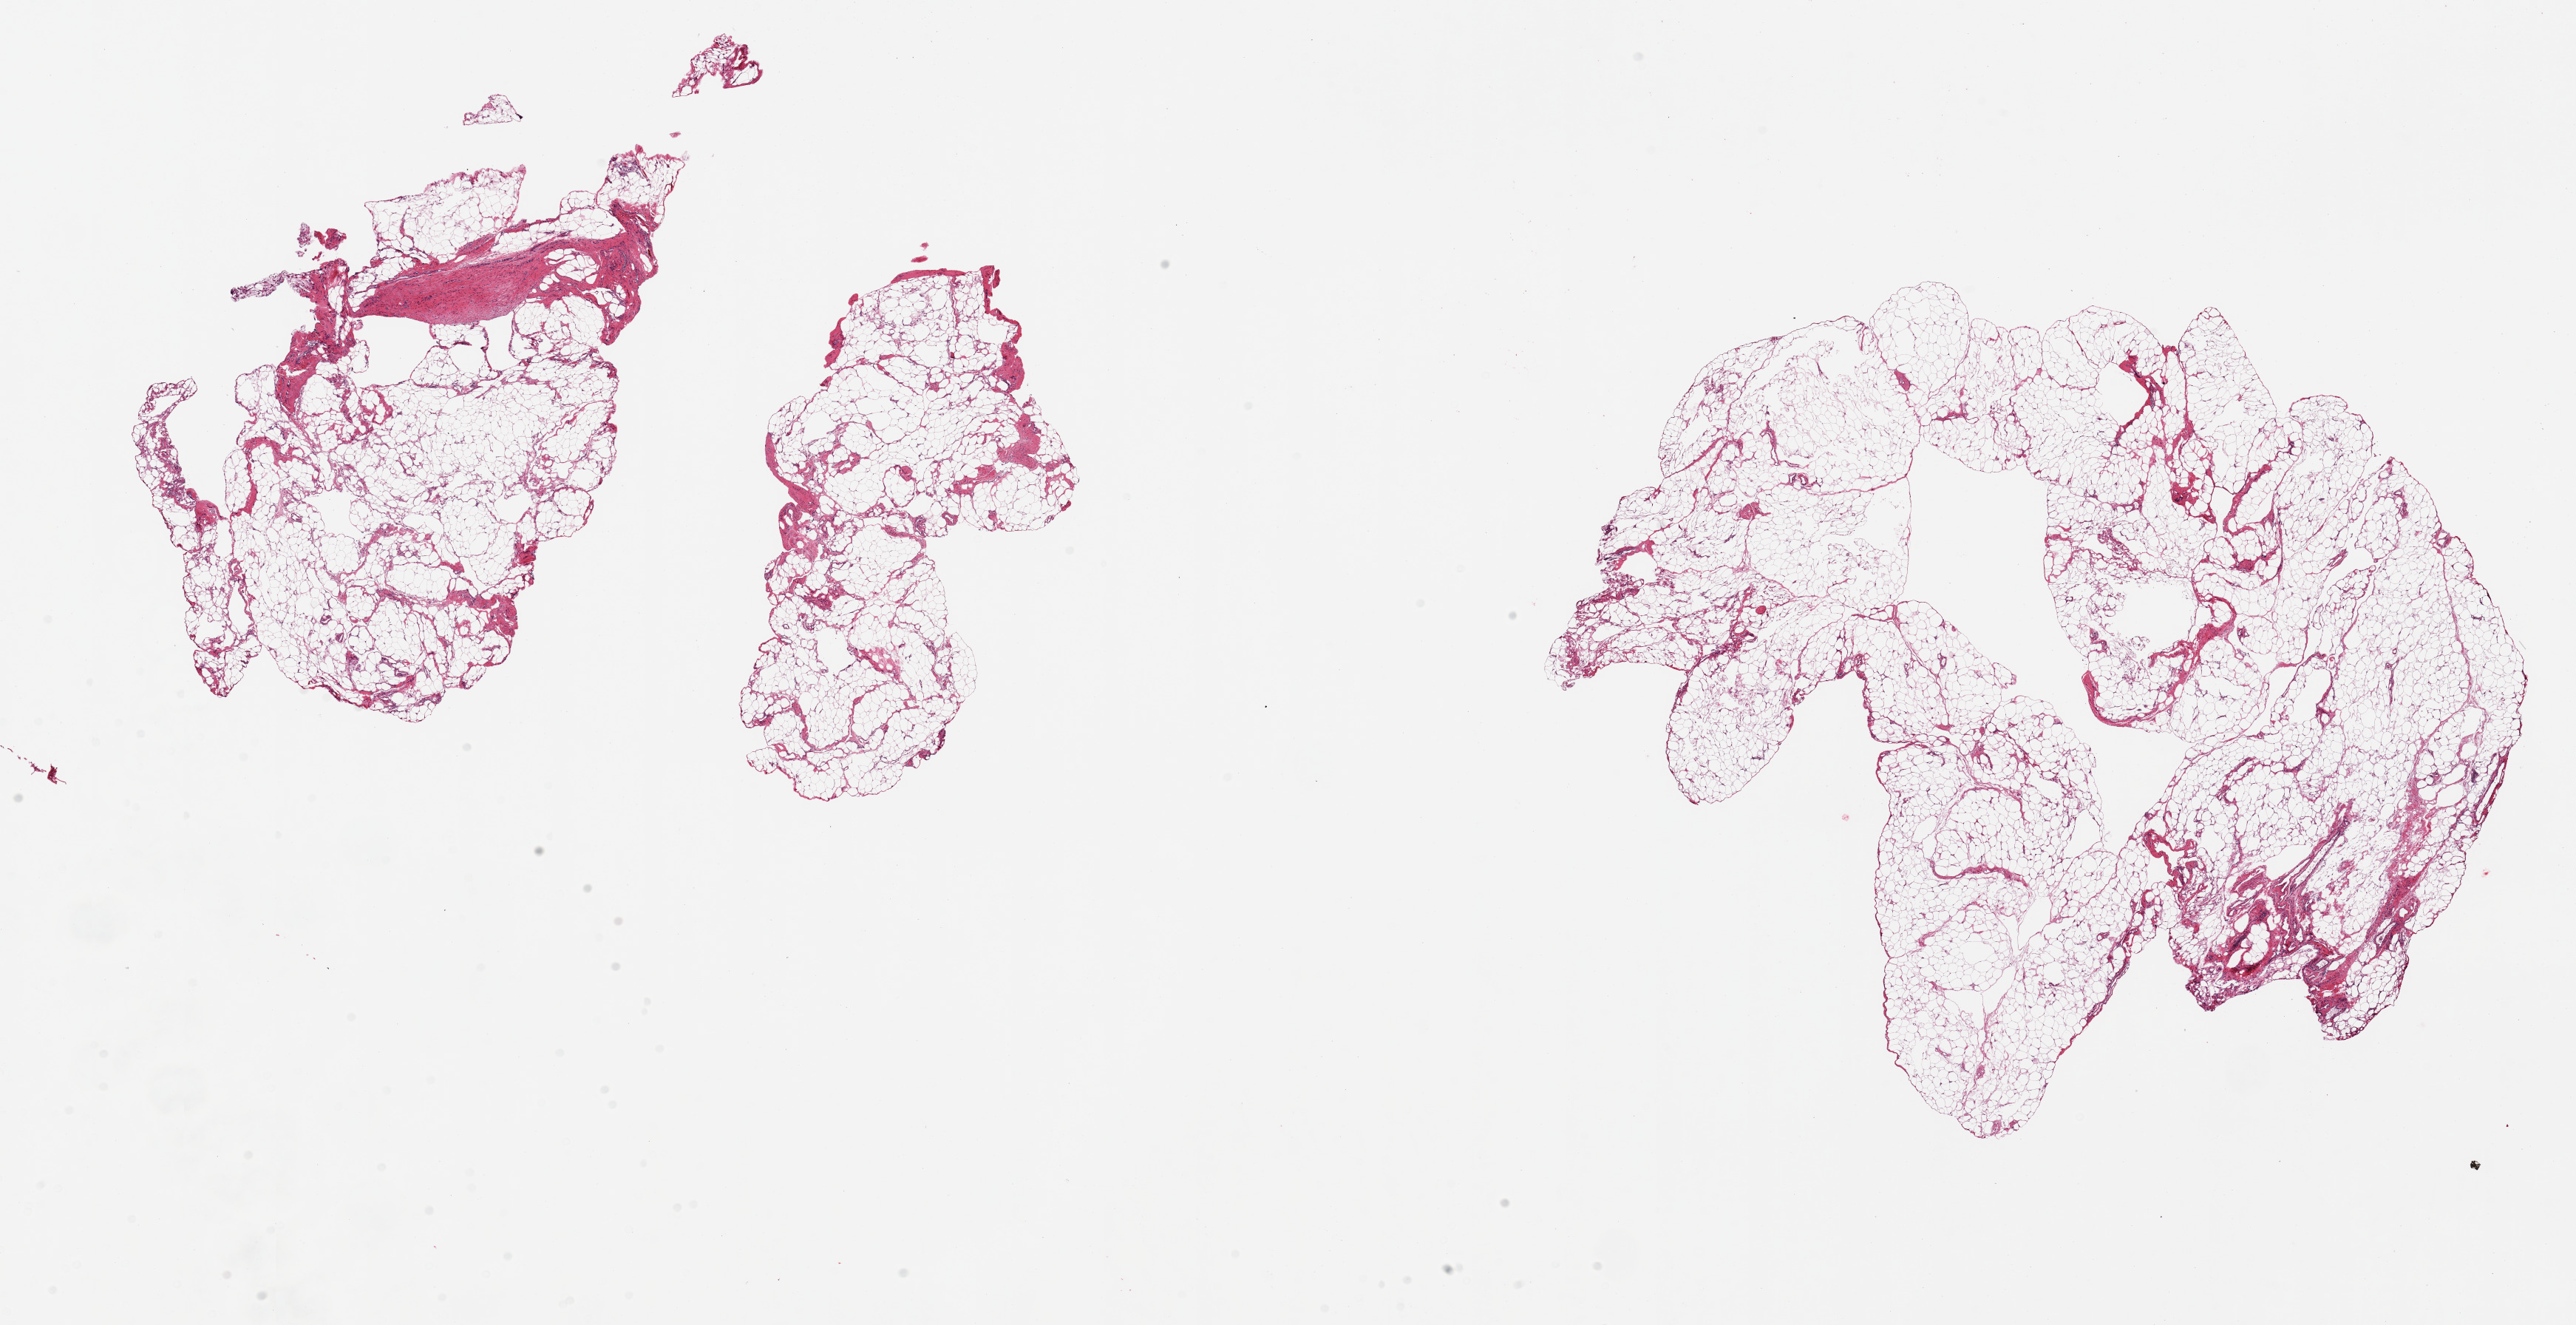
Whole-slide image, hematoxylin and eosin (H&E) stain, brightfield, whole scanned area (about 27.6 x 14.2 mm) shown as a low-resolution overview; PAXgene-fixed, paraffin-embedded tissue; section of omentum (target tissue); donor tissue sample. Female donor.
- review note (as recorded): 2 pieces, ~15-20% fascia/vascular elements